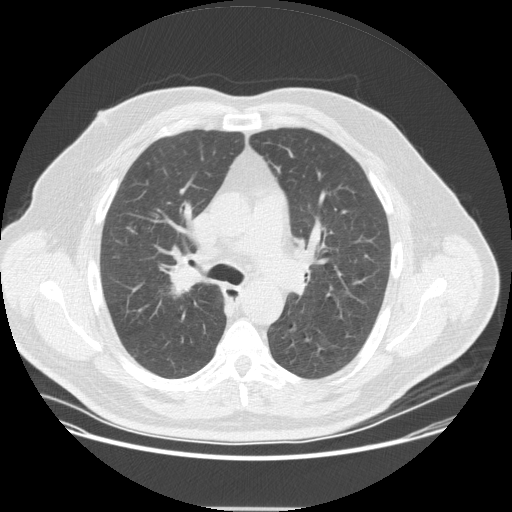
Low-dose screening chest CT, one axial slice. Position 228 of 351 along the scan axis. Reconstruction kernel STANDARD. 120 kVp. Lung window (W 1500 / L -600 HU). 2.5 mm slice thickness. 512 × 512 image matrix.
Annotated regions visible in this slice (manually delineated by an expert):
- lesion 1 (tumor, upper lobe of right lung): bounding box (x1, y1, x2, y2) in pixels: (167, 269, 203, 299)